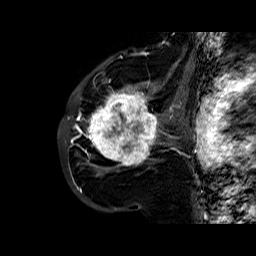
Breast MRI (dynamic contrast-enhanced), one sagittal slice; position 38 of 60 along the scan axis; dynamic contrast-enhanced series, time point 2 of 6 at this slice position (early post-contrast); 1.5 T; TE 6.4 ms, TR 32.8 ms; 256 × 256 image matrix, field of view 200 × 200 mm. Female patient. From the clinical record (not read from this slice): setting: breast cancer imaged before/during neoadjuvant chemotherapy; receptor status: HR-positive, HER2-negative.
Annotated regions visible in this slice (semi-automatically segmented with operator editing):
- analysis volume of interest (the breast-tissue region the enhancement analysis was run in; not a lesion): bounding box [x1, y1, x2, y2] px = [86, 77, 163, 177]
- tumour enhancement mask (voxels above the 100 % enhancement threshold inside the analysis volume of interest): [86, 81, 159, 166]